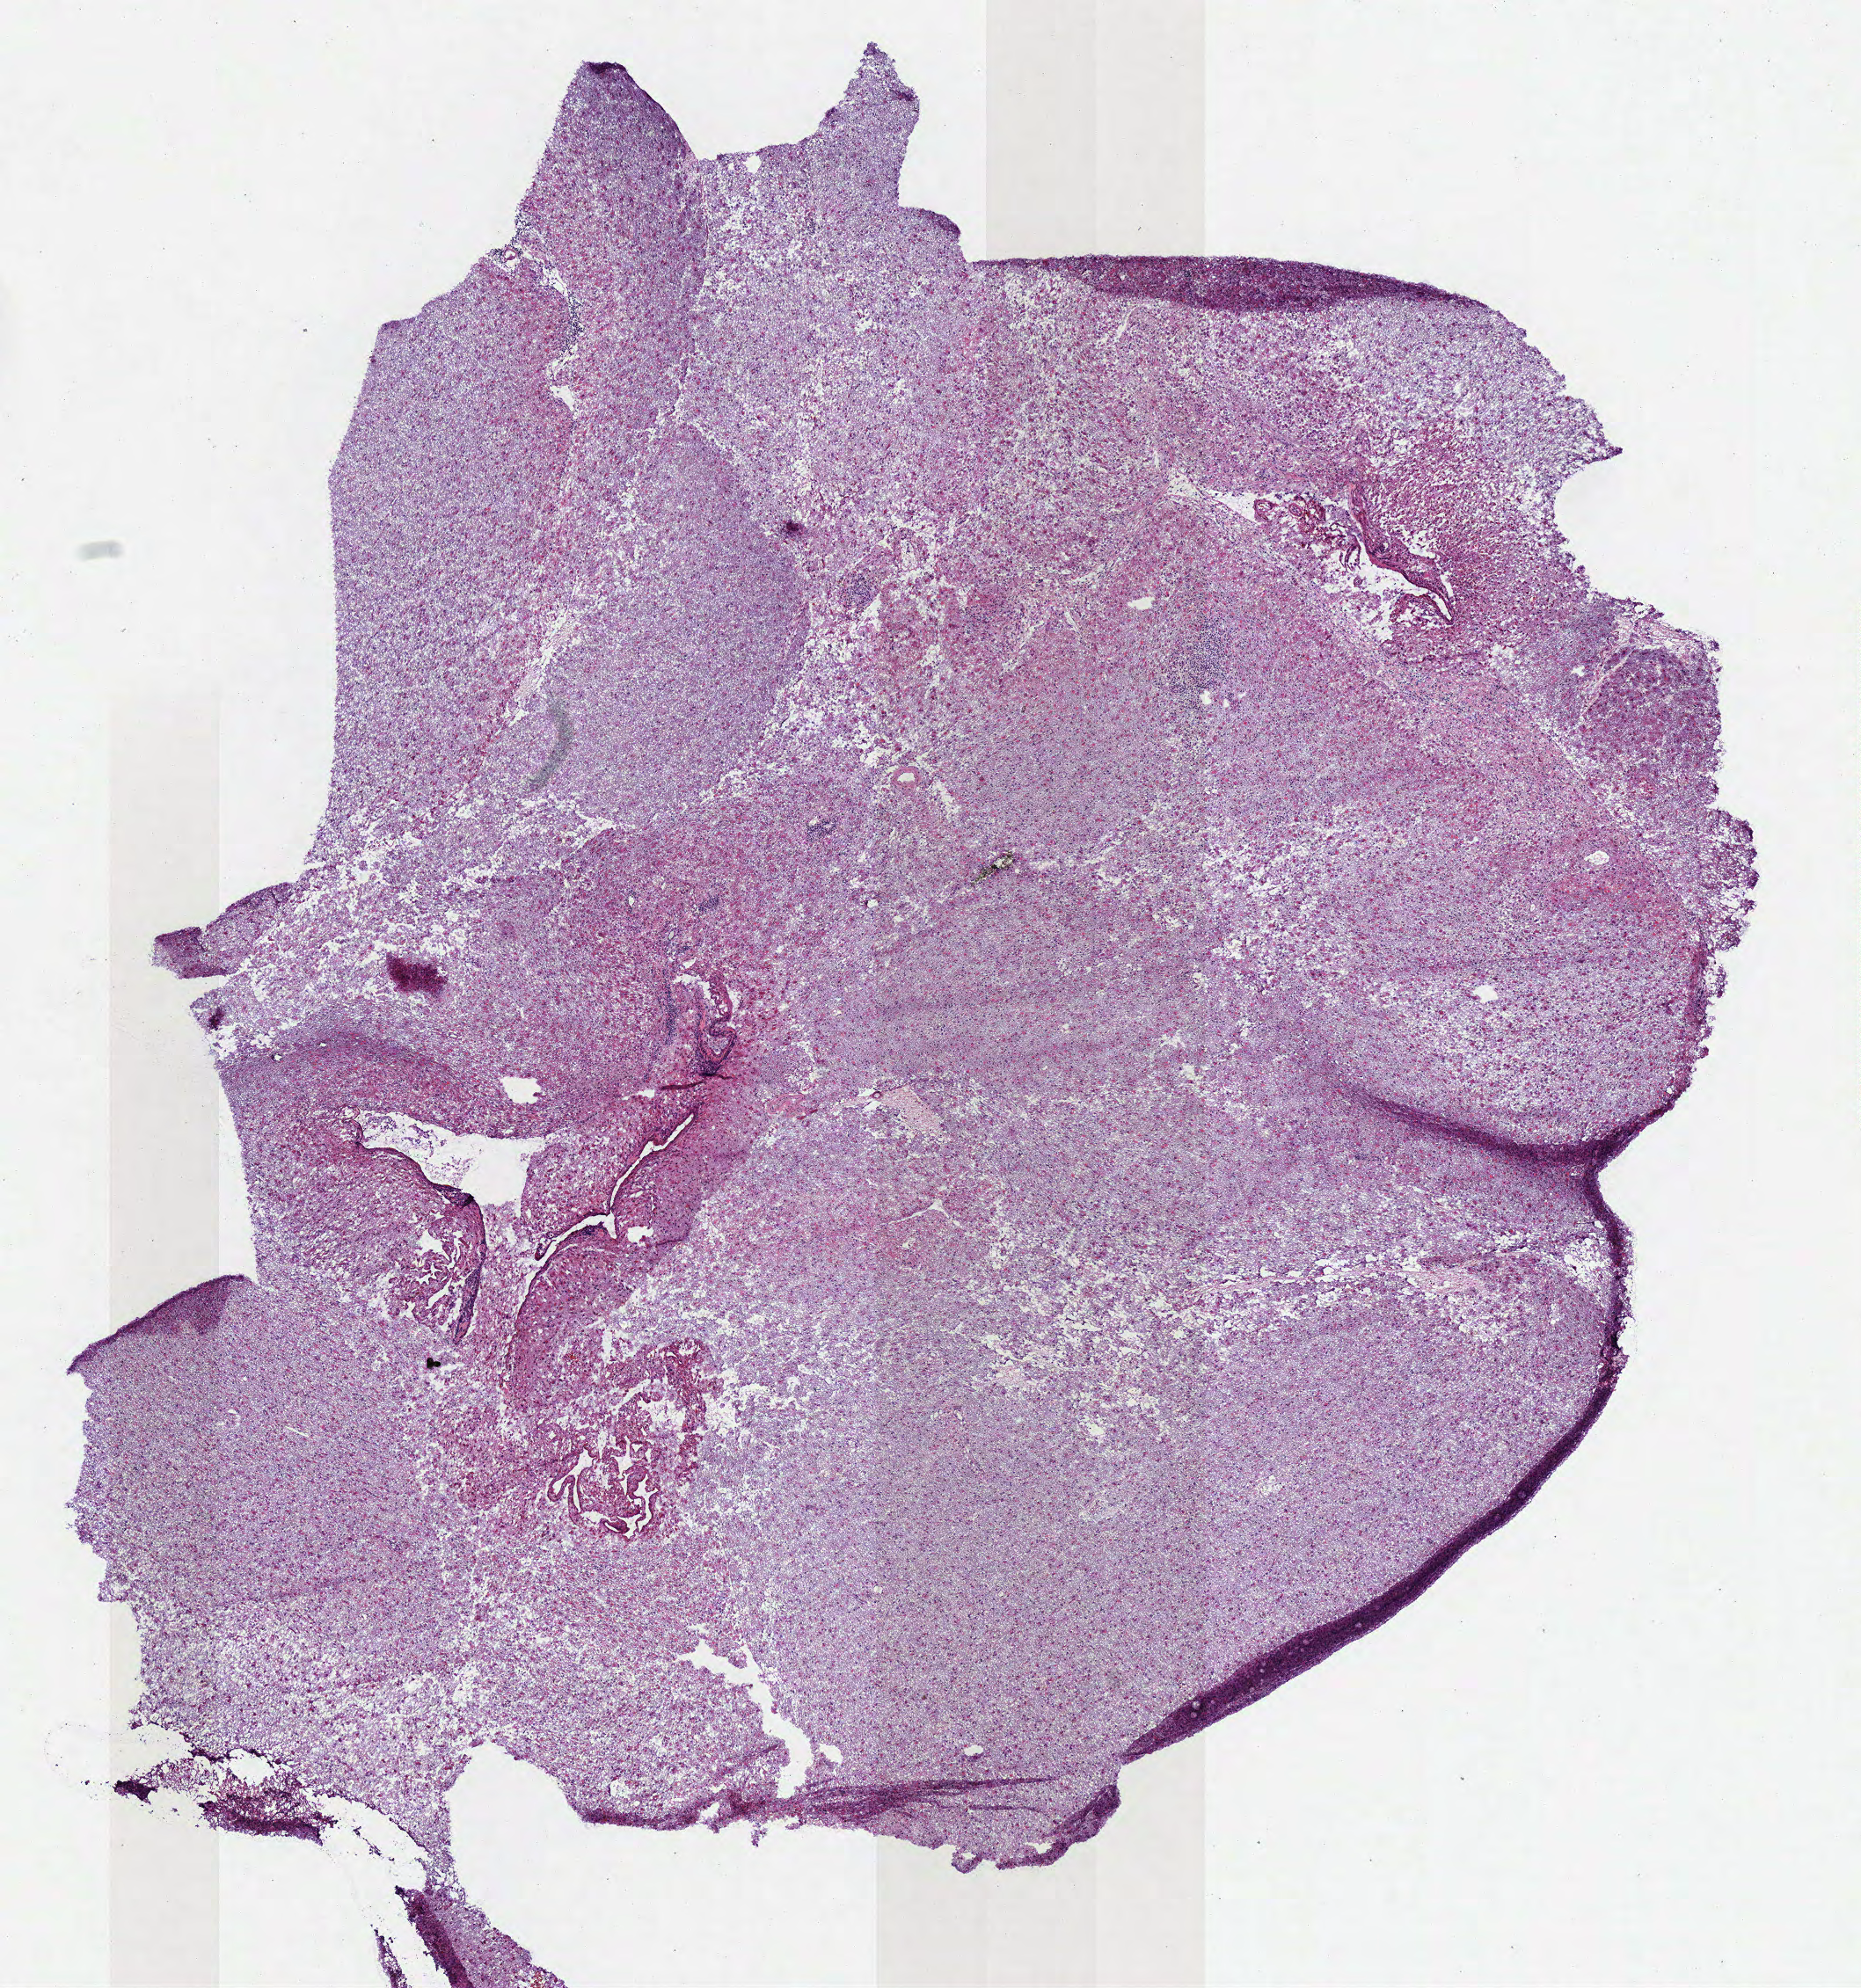
Whole-slide histology image, H&E — whole scanned area (about 8.3 x 8.9 mm, from a 40x scan) shown as a low-resolution overview. Frozen section from the bottom of the tissue portion. Brain, primary tumour sample. Female patient; age at initial diagnosis 74 years. Histologic grade: G3 (poorly differentiated). Composition of this section per pathologist review: tumour cells 100%, tumour nuclei 75%, normal cells 0%, stromal cells 0%, necrosis 0%.
• laterality: left
• pathologic diagnosis: Astrocytoma, anaplastic (cerebrum)